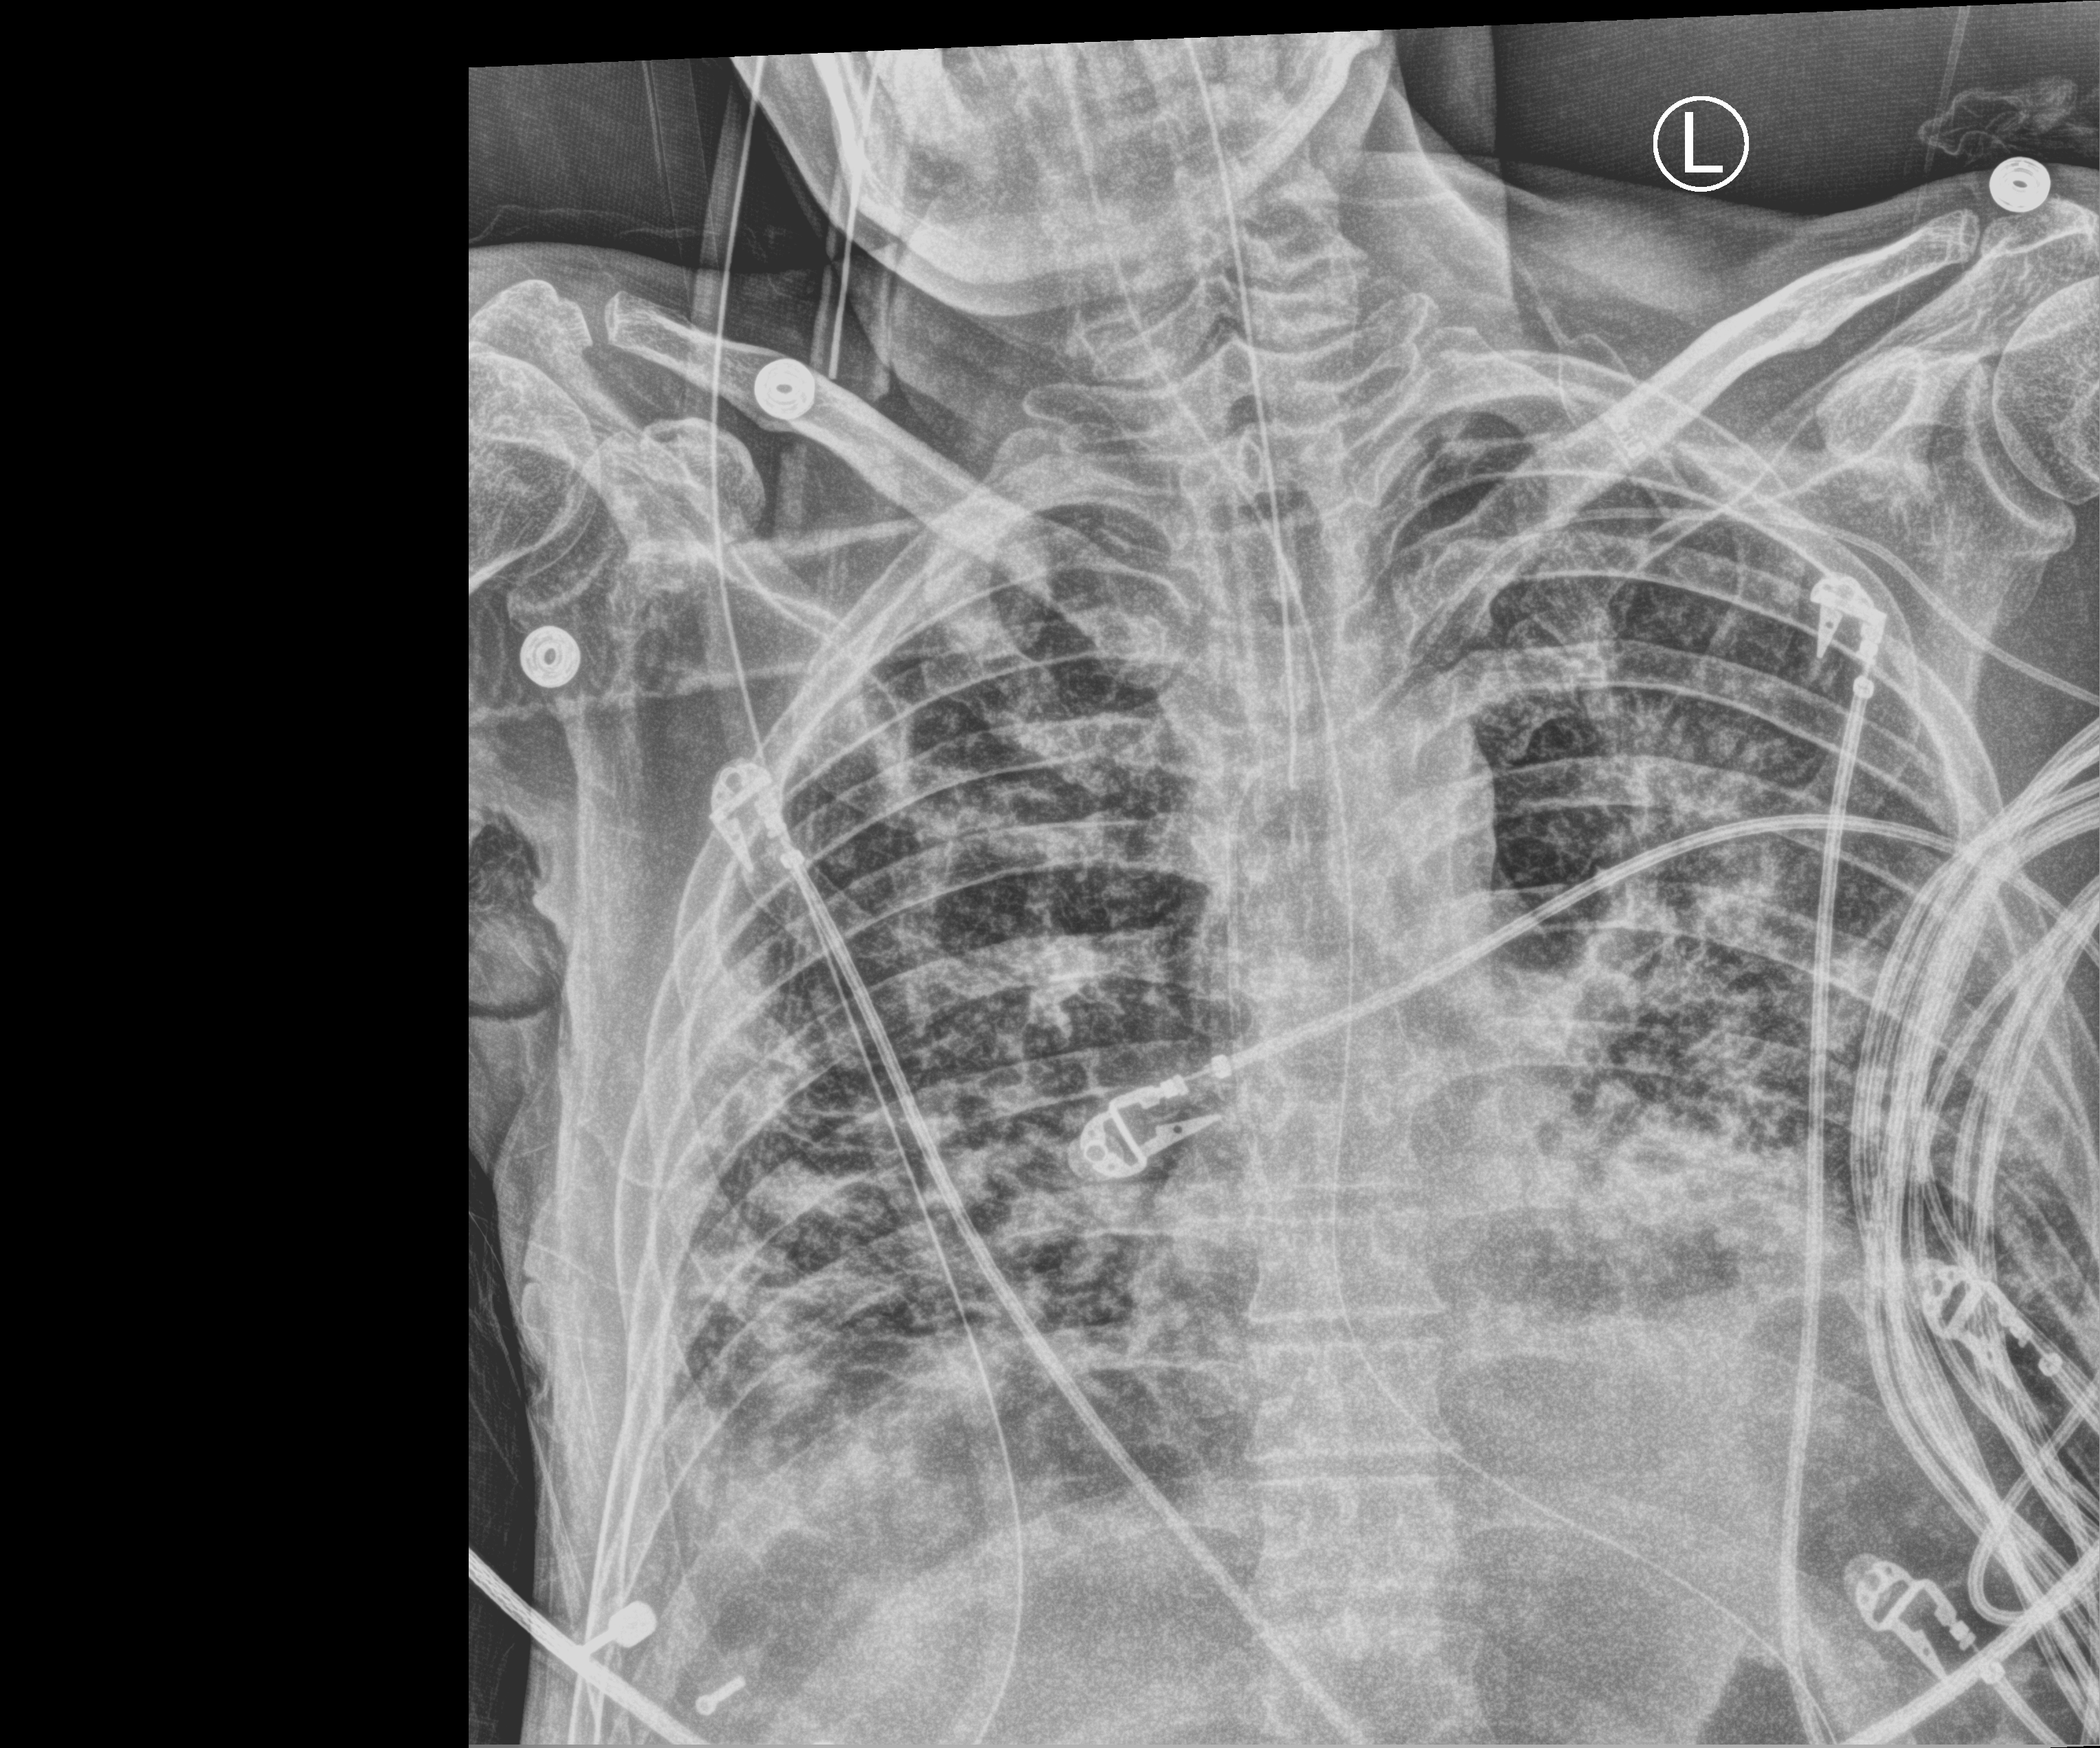
Chest X-ray (portable); anteroposterior (AP) projection. Male patient hospitalised with COVID-19, age 18–59 years.
From the hospital-stay record, not from the radiograph (when in the stay this image was taken is not recorded): admitted to intensive care during this hospital stay: yes; diabetes (admission record): yes; COPD (admission record): no.